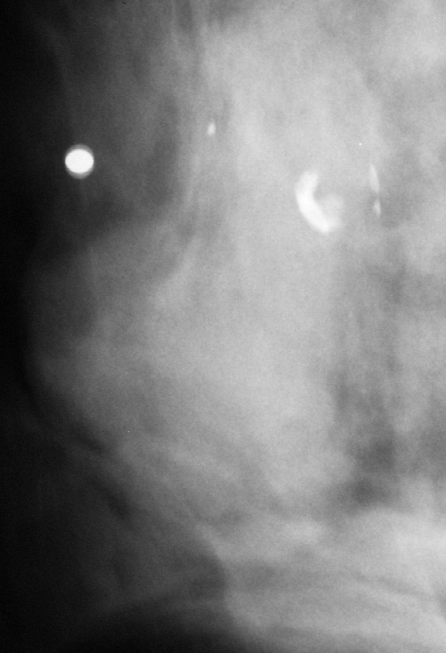
Crop from a digitized film mammogram around one marked abnormality; right breast; MLO view.
Mass, shape oval, margins circumscribed; BI-RADS assessment category 3; pathology result (as recorded, not read from the image): benign.